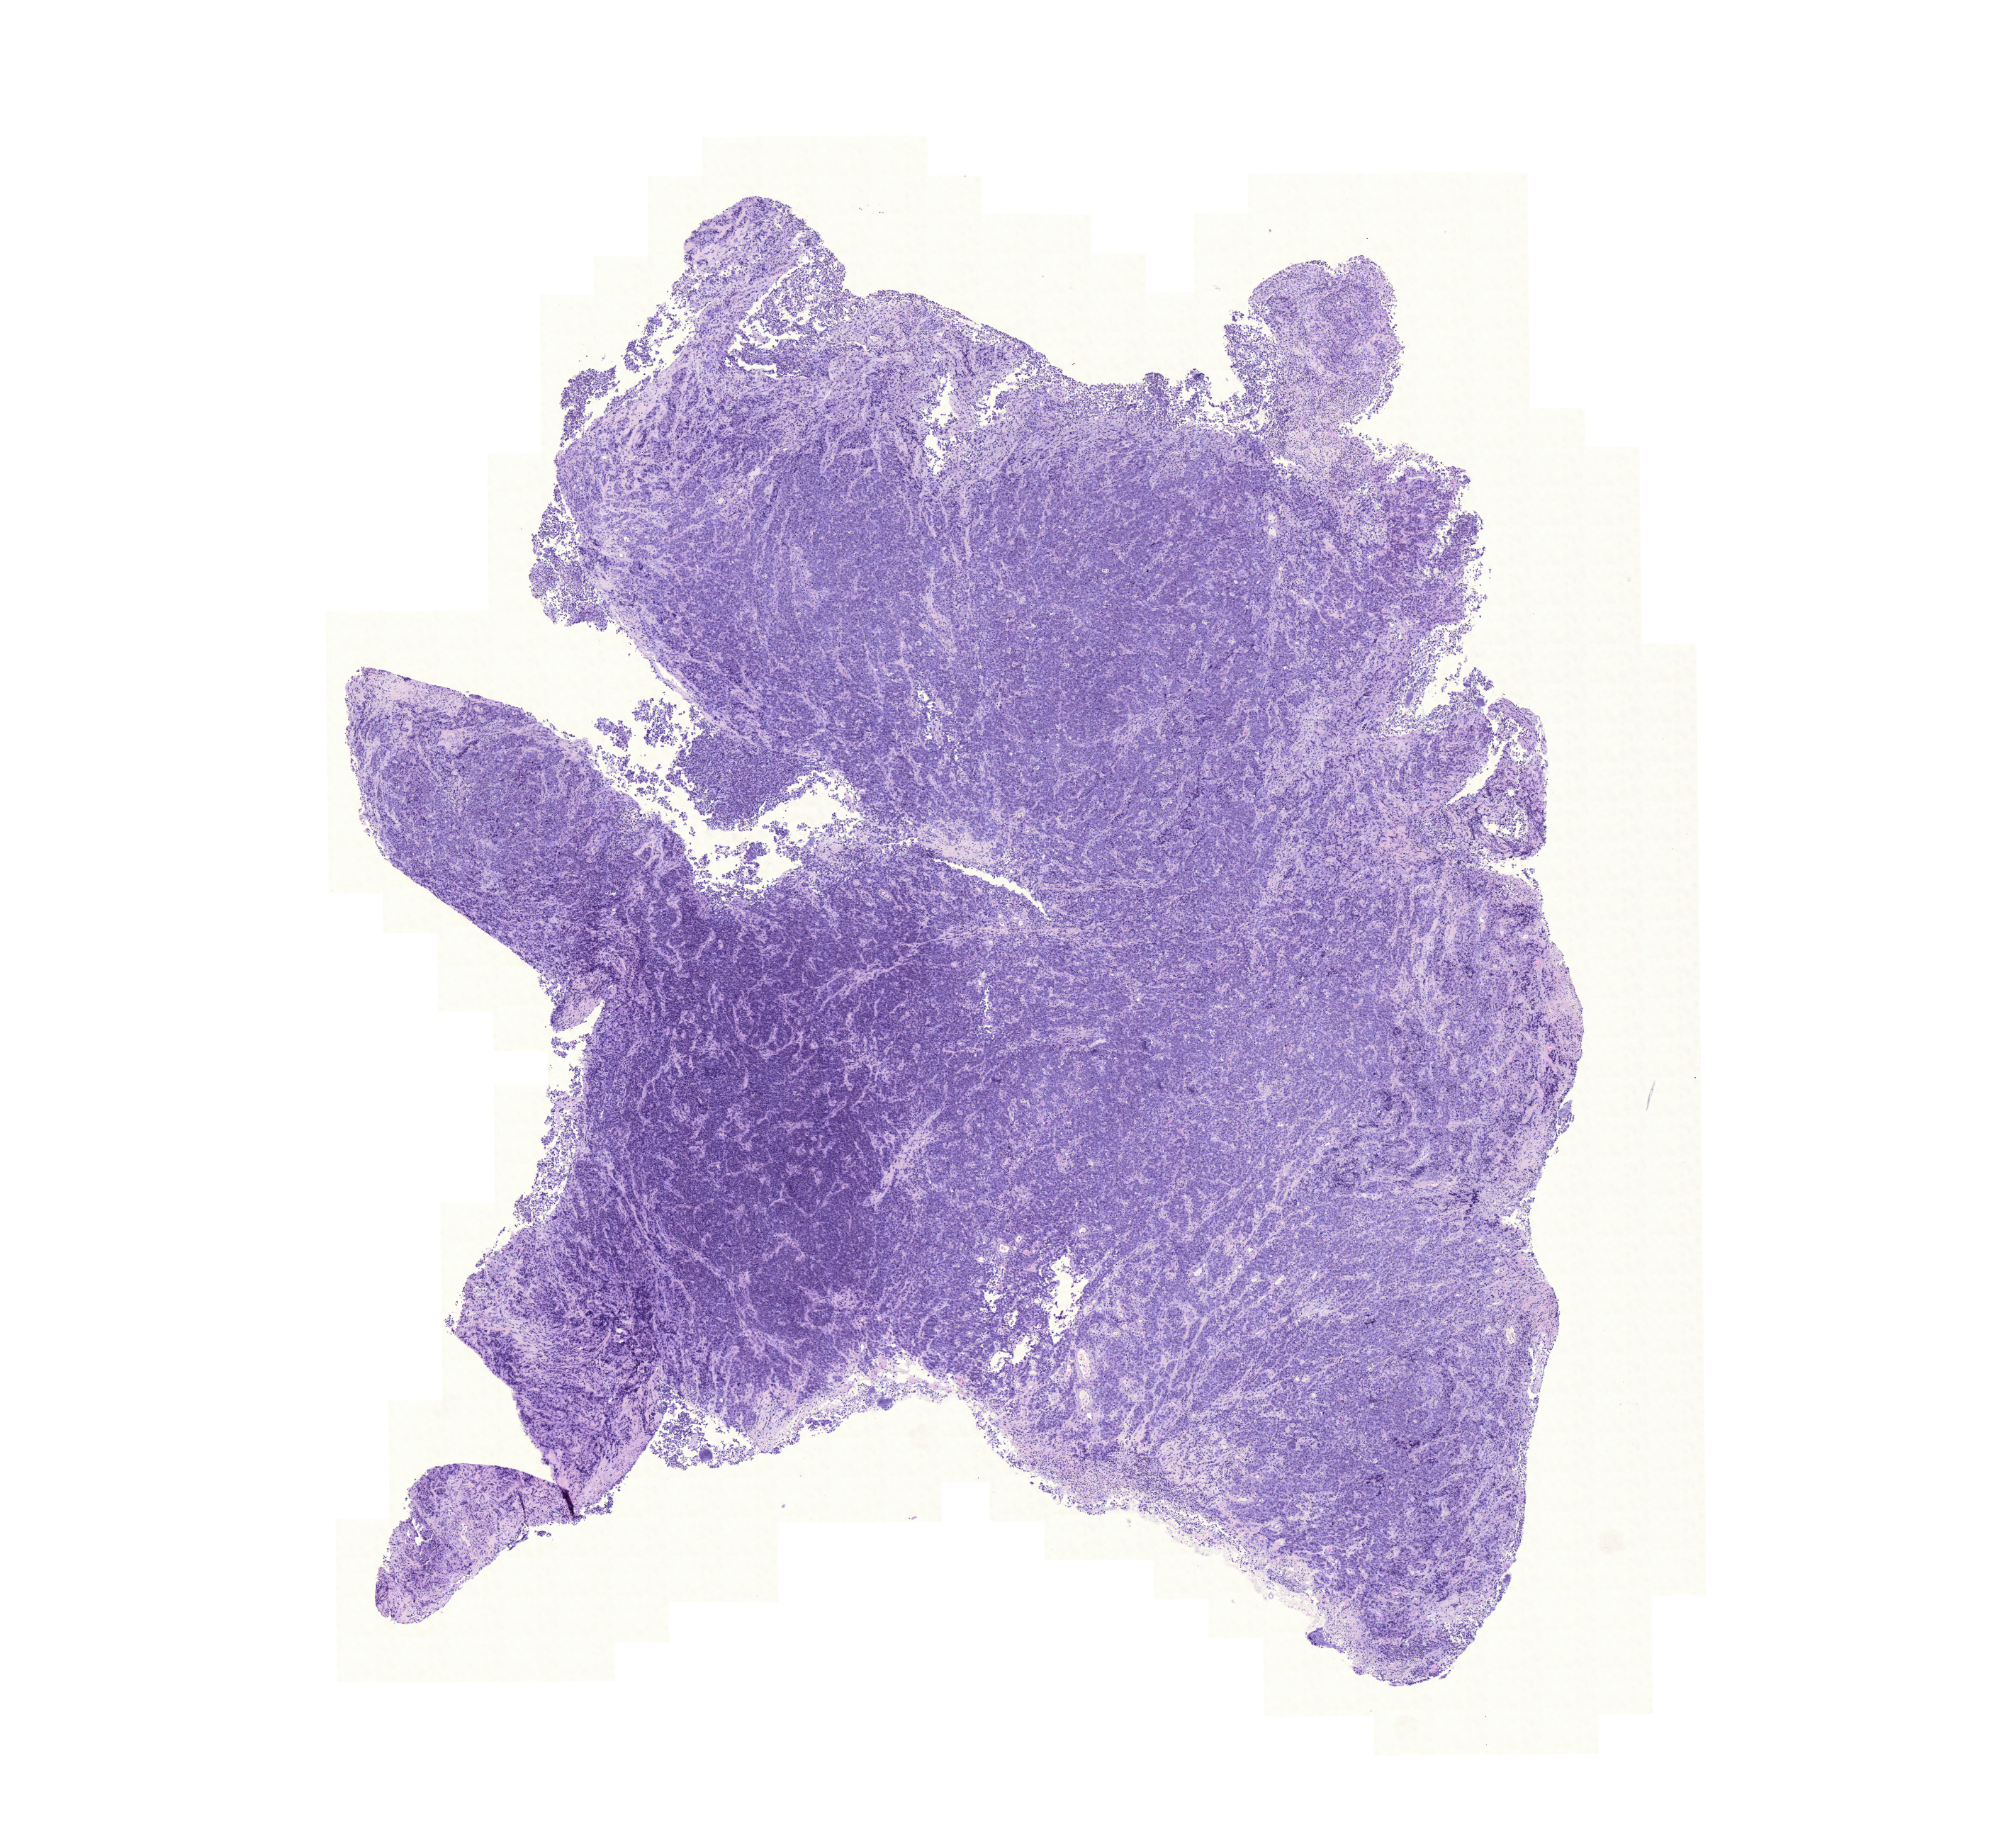
H&E whole-slide image — low-resolution overview of the scanned area, about 10.5 x 9.7 mm (acquisition: 20x scan). Formalin-fixed paraffin-embedded (FFPE) diagnostic section. Colon, primary tumour sample. Patient: female, age at initial diagnosis 64 years.
Pathologic diagnosis: Adenocarcinoma, NOS (cecum). AJCC pathologic stage: I (6th edition). Lymph nodes positive (case pathology): 0 of 27 examined.